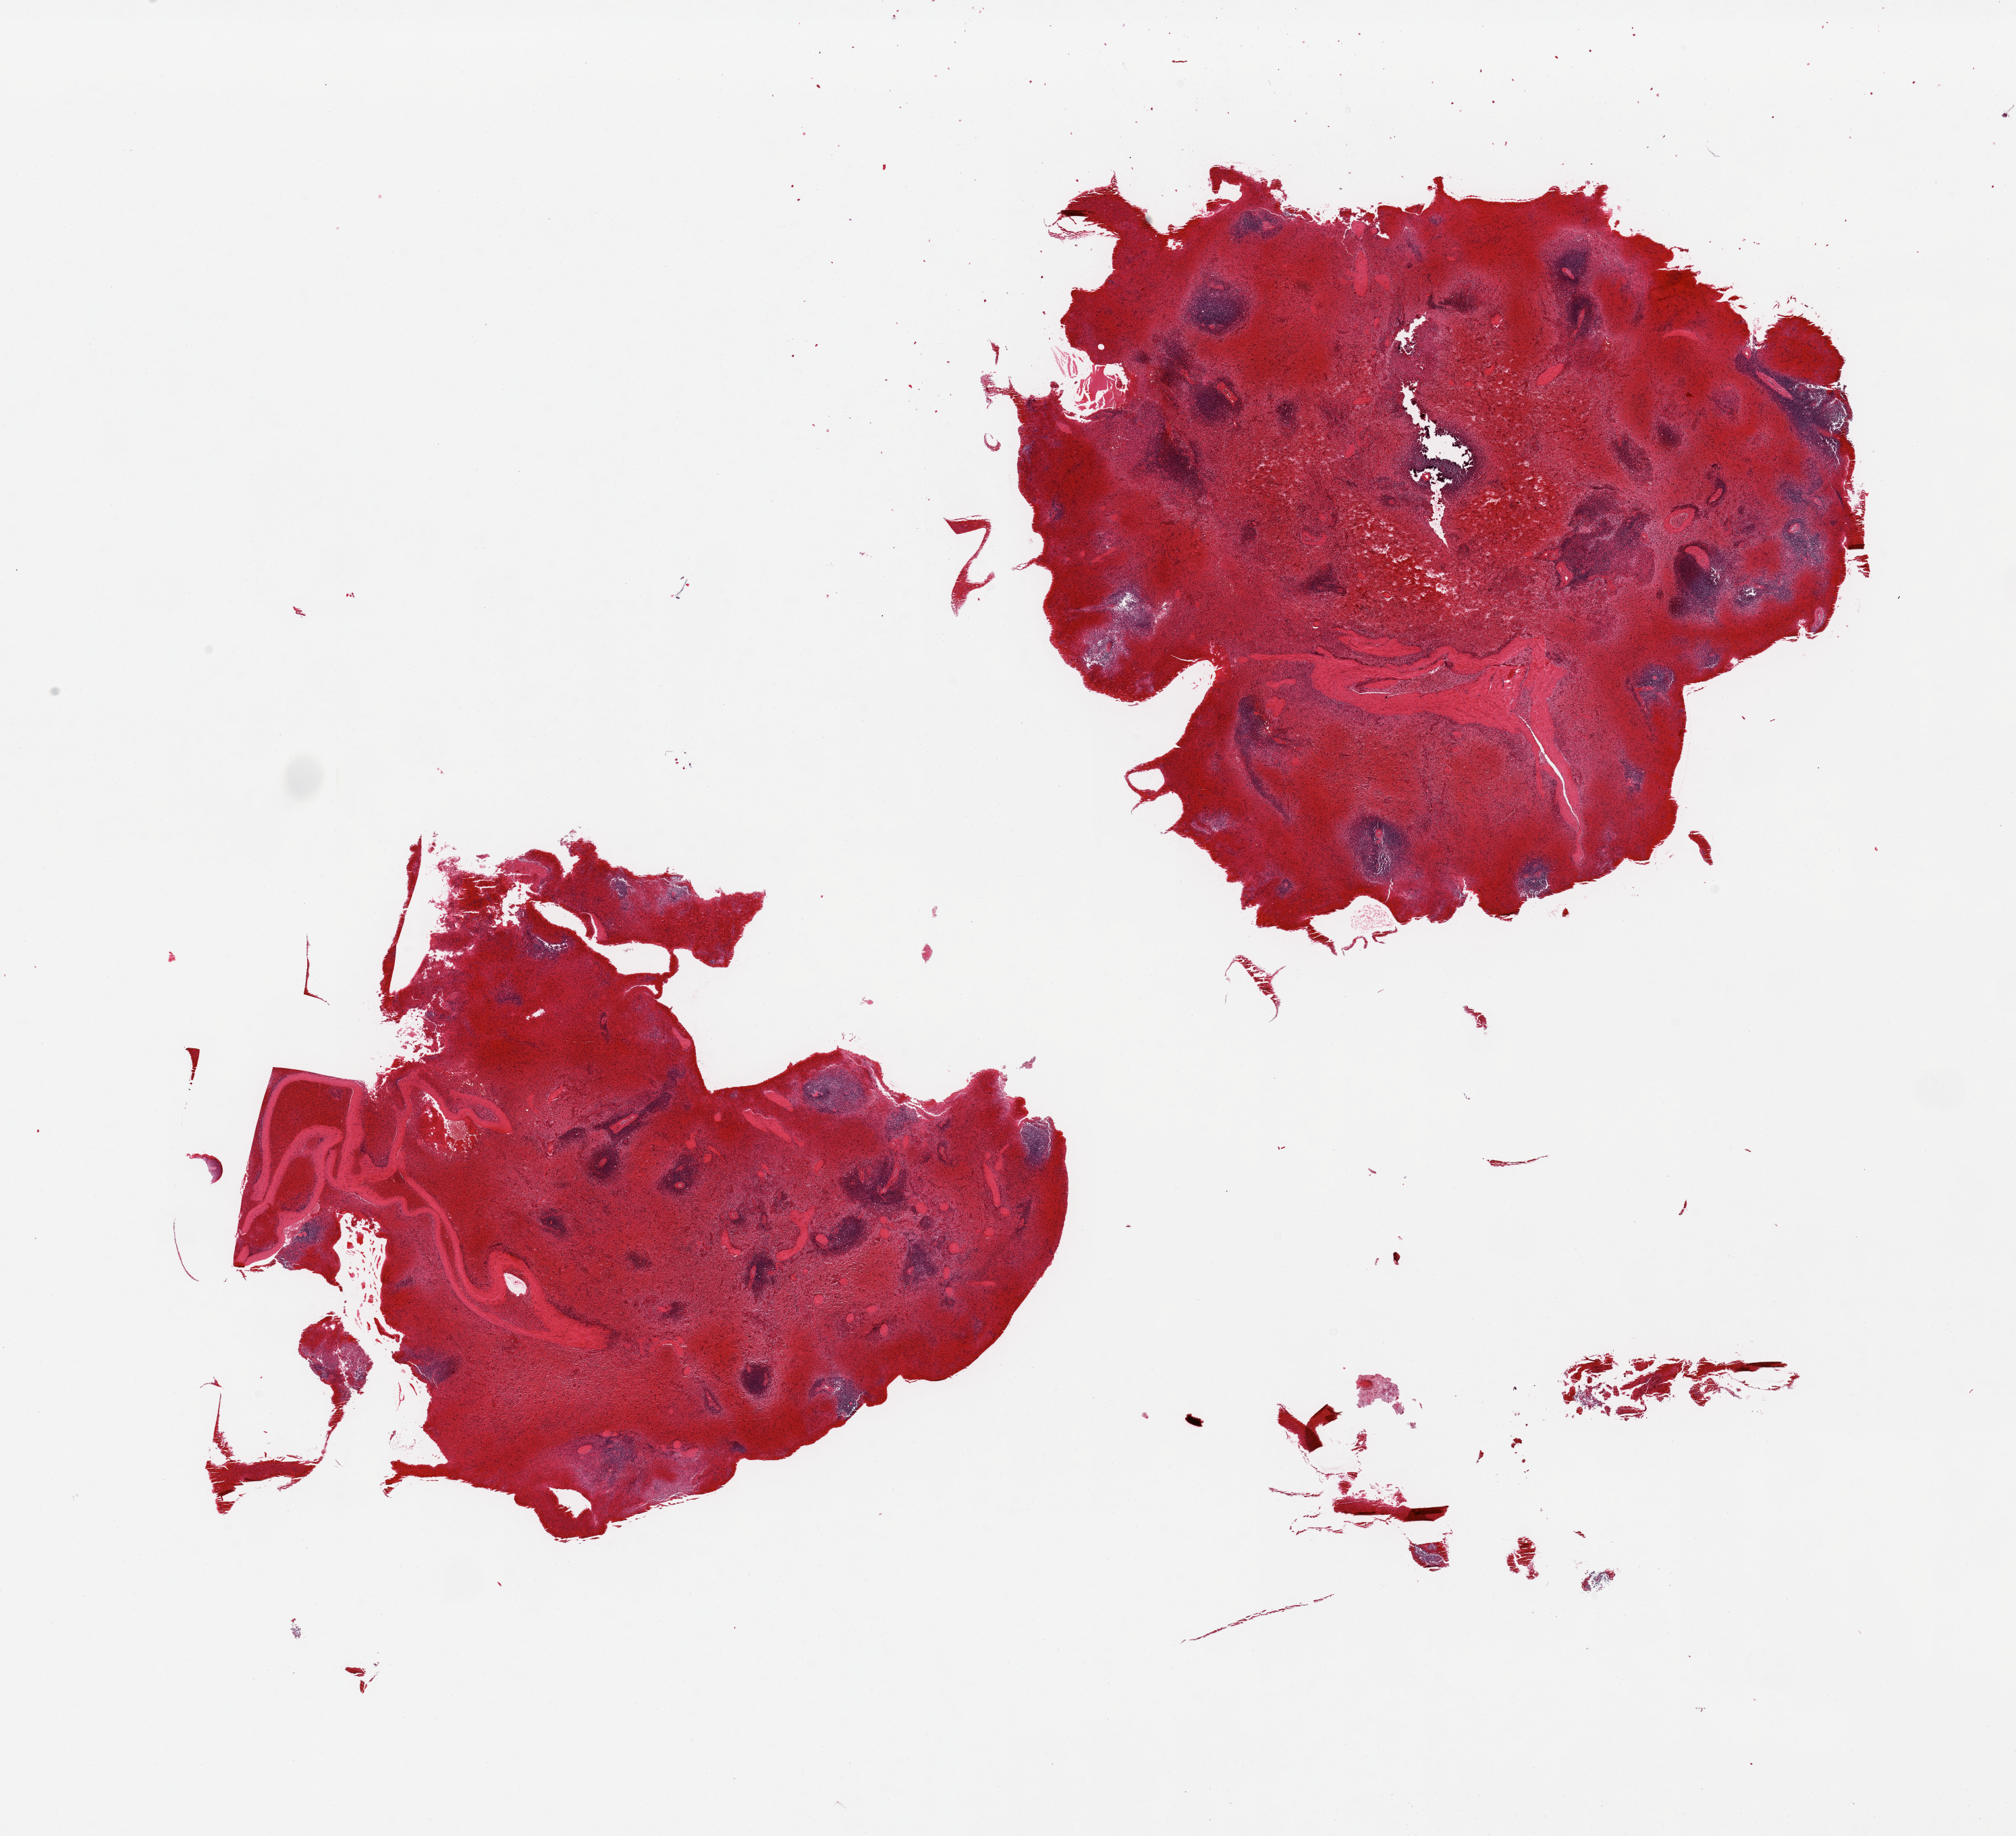
Hematoxylin and eosin (H&E) whole-slide image, brightfield, whole scanned area (about 23.6 x 21.5 mm, slide scanned at 20x) shown as a low-resolution overview; PAXgene-fixed paraffin-embedded (PFPE) section; target tissue: spleen; donor tissue sample. Male donor.
Pathologist's review note for this sample: 6 pieces; acute vascular congestion.